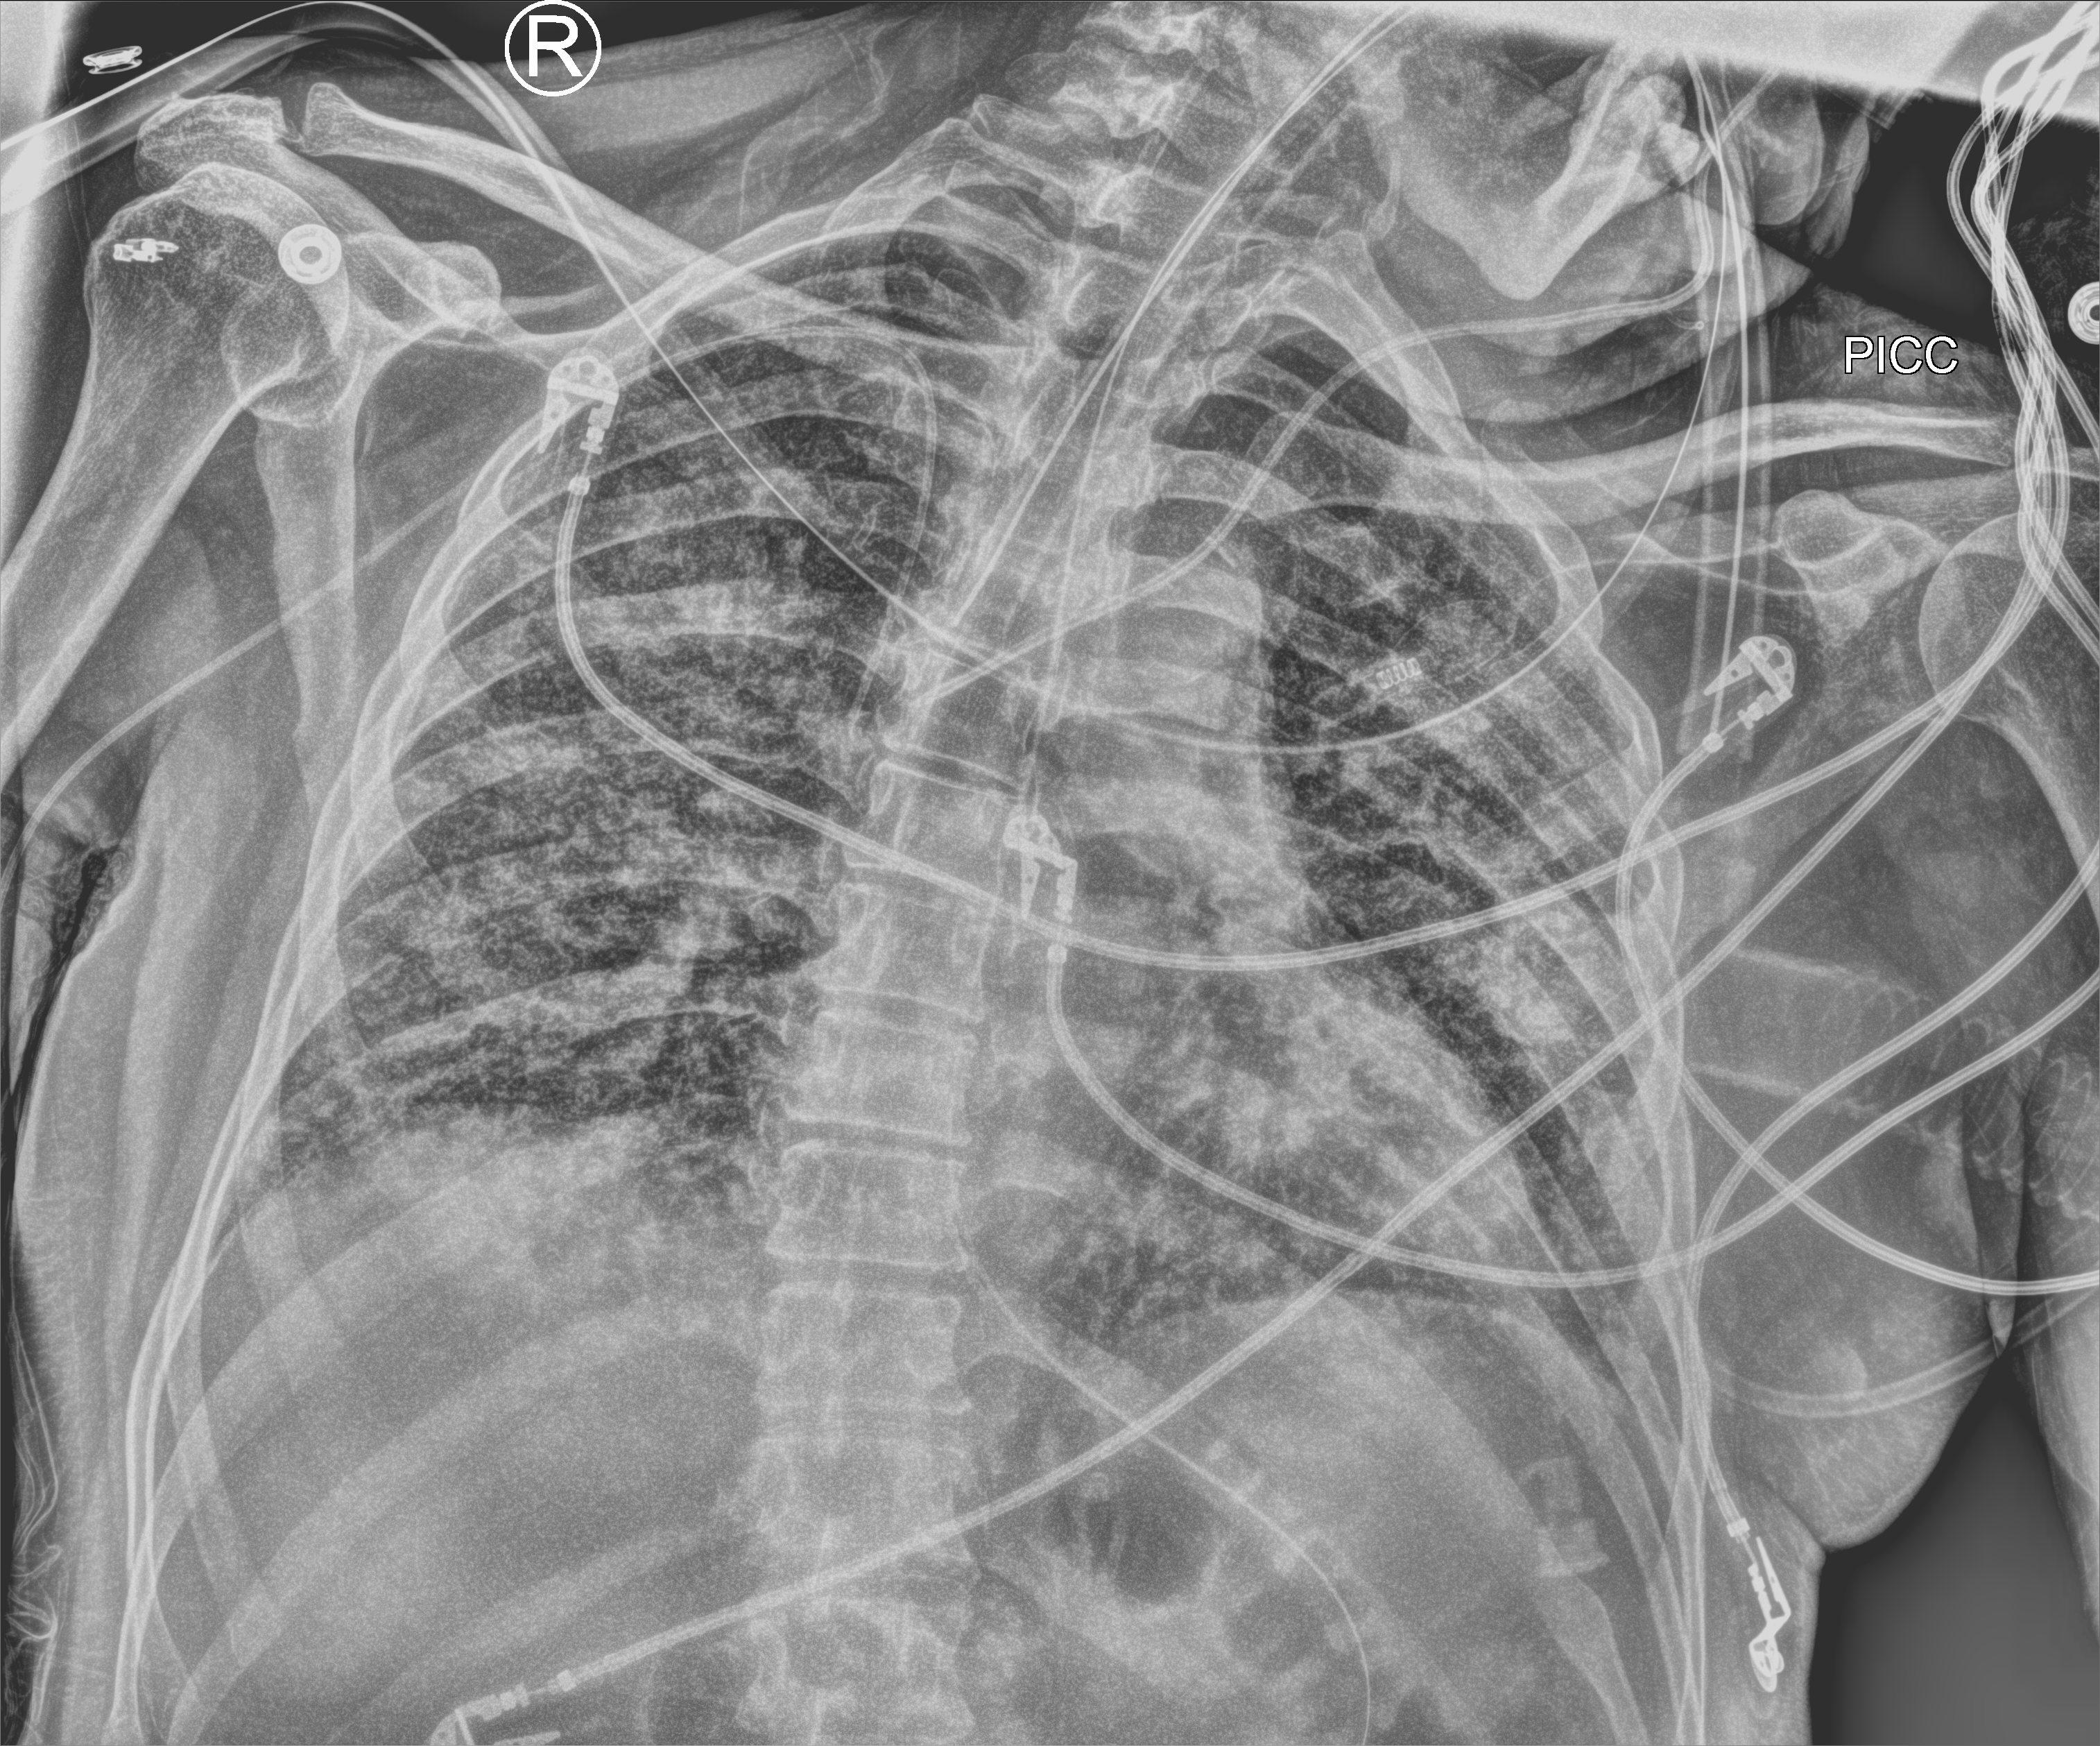
Portable chest radiograph, anteroposterior (AP) projection. Male patient hospitalised with COVID-19, age 60–74 years.
From the hospital-stay record, not from the radiograph (when in the stay this image was taken is not recorded): mechanically ventilated during this hospital stay: yes; admitted to intensive care during this hospital stay: yes.